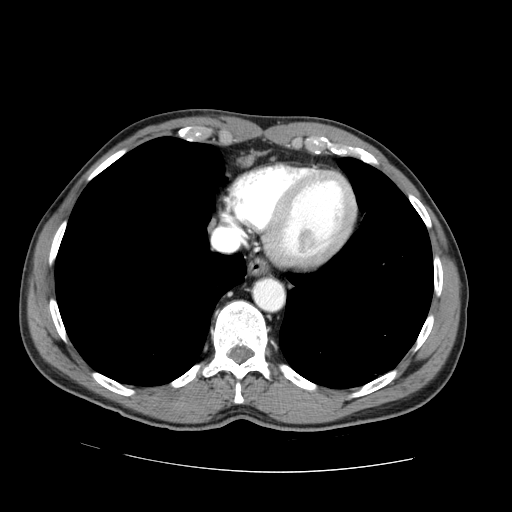
Contrast-enhanced abdominal CT (liver protocol), one axial slice. Position 68 of 73 along the scan axis. 100 kVp. One of 2 acquisitions stored at this slice position. Soft-tissue window (W 400 / L 40 HU). 512 × 512 image matrix, field of view 380 × 380 mm. From the clinical record (not read from this slice): diagnosis: hepatocellular carcinoma (patient treated with transarterial chemoembolisation; whether this scan precedes or follows treatment is not stated here); TNM stage (as recorded): Stage-IVA; Child-Pugh class: A; tumour nodularity: uninodular.
Annotated regions visible in this slice (semi-automatic segmentation, software-assisted and operator-edited):
- abdominal aorta: box from (x=254, y=280) to (x=283, y=311) px